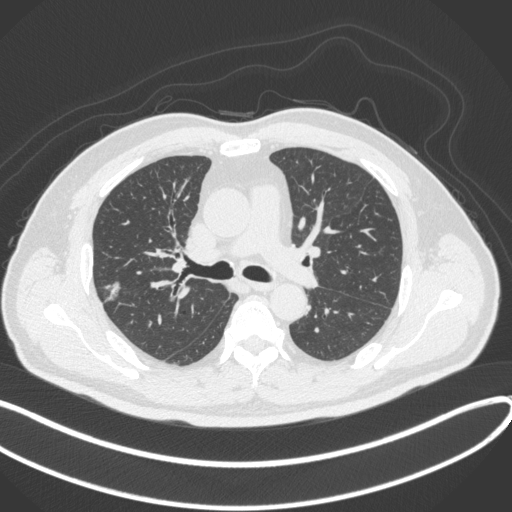
Chest CT, one axial slice. Position 213 of 373 along the scan axis. Reconstruction kernel B31f. Lung window (W 1500 / L -600 HU). 1 mm slice thickness. 512 × 512 image matrix, field of view 400 × 400 mm. Male patient, age 60 years. Case-level facts recorded for this patient, not image findings: clinical TNM (as recorded): T1c N0 M0.
Structures marked on this image (bounding box drawn by a radiologist):
- lung tumour (recorded histology: adenocarcinoma): box from (x=98, y=274) to (x=121, y=308) px